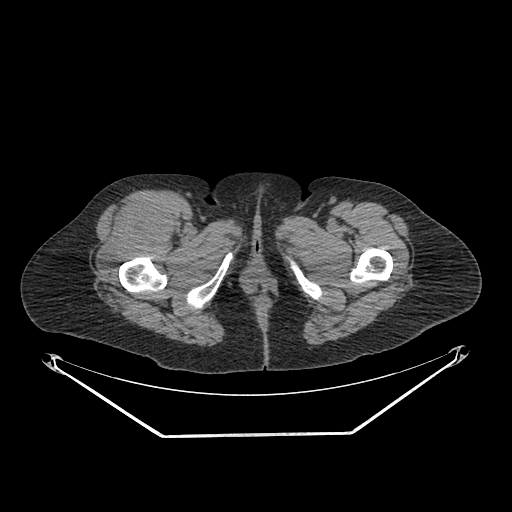
CT of an extremity soft-tissue mass (from a PET/CT study), one axial slice; slice 278 of 311 in the series (ordered by position); reconstruction kernel SOFT; 140 kVp; soft-tissue window (W 400 / L 40 HU); 3.75 mm slice thickness; 512 × 512 image matrix, field of view 500 × 500 mm. Female patient. Case-level facts recorded for this patient, not image findings: histological type: pleiomorphic undifferentiated sarcoma; grade: high; site of the primary tumour: right quadricep.
Annotated regions visible in this slice (expert contour drawn on MRI and transferred to this co-registered scan by the dataset authors):
- tumour plus oedema (research contour): bounding box <100,199,170,271> (left, top, right, bottom; pixels)
- tumour (research contour): <100,199,170,271>